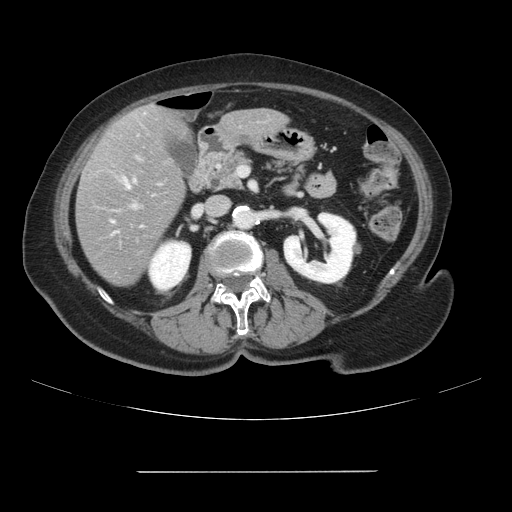
Contrast-enhanced abdominal CT, one axial slice; slice 36 of 111 in the series (ordered by position); 120 kVp; intravenous contrast given; soft-tissue window (W 400 / L 40 HU); 2.5 mm slice thickness; 512 × 512 image matrix. Female patient, age 74 years. Case-level facts recorded for this patient, not image findings: diagnosis: colorectal cancer liver metastases, imaged before liver resection; multiple liver metastases: yes; largest metastasis: 1.1 cm; disease in both lobes: yes.
Annotated regions visible in this slice (expert manual segmentation):
- hepatic veins: box from (x=124, y=180) to (x=129, y=187) px
- liver: (x=77, y=105)–(x=286, y=285)
- planned liver remnant (the part of the liver to remain after resection): (x=140, y=105)–(x=266, y=140)